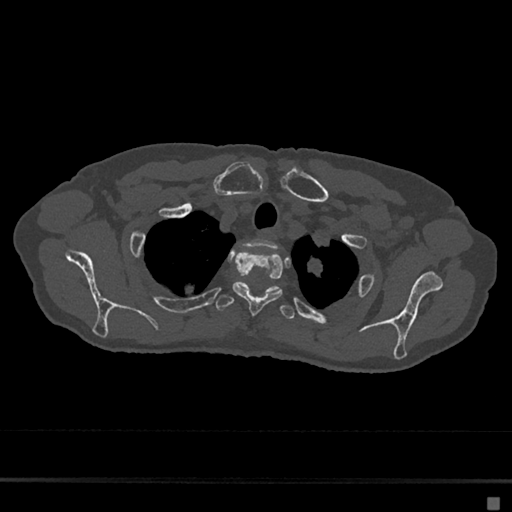
CT including the spine, one axial slice; position 567 of 797 along the scan axis; reconstruction kernel Br40s/3; bone window (W 1800 / L 400 HU); 512 × 512 image matrix. Female patient, age 68 years. Case-level facts recorded for this patient, not image findings: primary cancer: renal.
Structures marked on this image (semi-automatically segmented with operator editing):
- T1 vertebra: box from (x=248, y=239) to (x=277, y=250) px
- T2 vertebra: (x=232, y=251)–(x=283, y=315)
- T3 vertebra: (x=215, y=281)–(x=296, y=320)